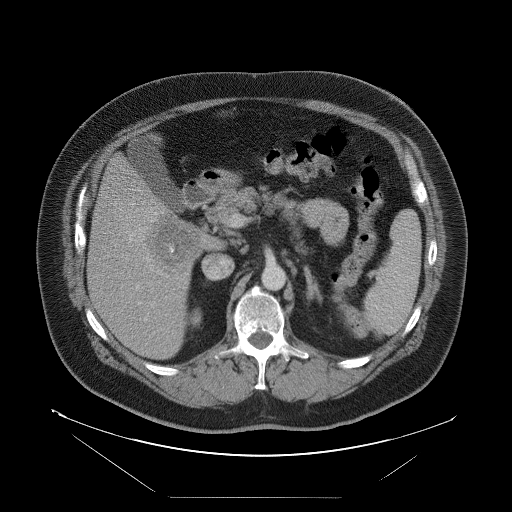
Contrast-enhanced abdominal CT, one axial slice; position 49 of 114 along the scan axis; 120 kVp; soft-tissue window (W 400 / L 40 HU); 5 mm slice thickness; 512 × 512 image matrix, field of view 500 × 500 mm. Male patient, age 61 years. Case-level facts recorded for this patient, not image findings: diagnosis: colorectal cancer liver metastases, imaged before liver resection; multiple liver metastases: no; largest metastasis: 6.5 cm; disease in both lobes: yes.
Annotated regions visible in this slice (expert manual segmentation):
- liver: bounding box [x1, y1, x2, y2] px = [89, 158, 219, 359]
- liver metastasis: [149, 215, 202, 266]